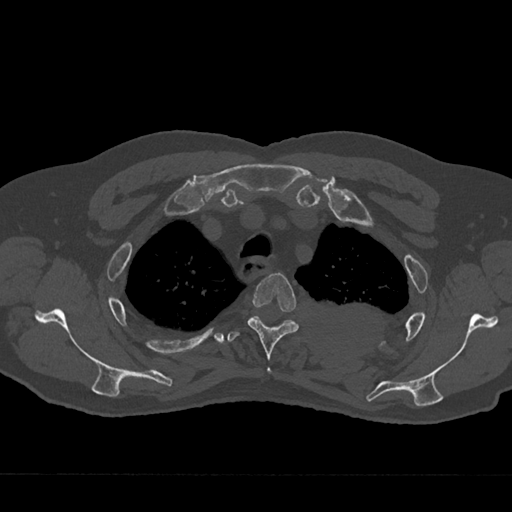
CT including the spine, one axial slice. 120 kVp. Bone window (W 1800 / L 400 HU). 0.5 mm slice thickness. 512 × 512 image matrix, field of view 377 × 377 mm. Patient: male, 75 years. From the clinical record (not read from this slice): primary cancer: renal; vertebrae with lytic lesions (as recorded): T4.
Outlined on this slice (semi-automatic segmentation, software-assisted and operator-edited):
- T3 vertebra: box from (x=247, y=272) to (x=299, y=373) px
- T4 vertebra: (x=227, y=316)–(x=294, y=342)